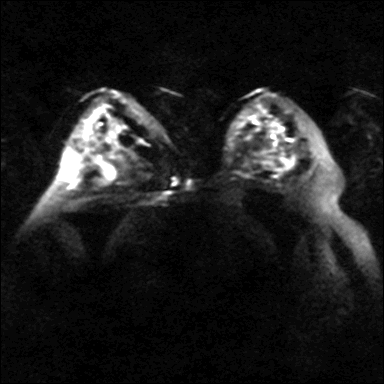
Breast MRI, one axial slice; diffusion-weighted series; image 2 of 4 stored at this slice position (different b-values; order by instance number); 3 T; 4 mm slice thickness; 384 × 384 image matrix, field of view 320 × 320 mm. Female patient.
Outlined on this slice (expert manual segmentation):
- tumour on diffusion-weighted imaging: bounding box [x1, y1, x2, y2] px = [269, 118, 281, 134]